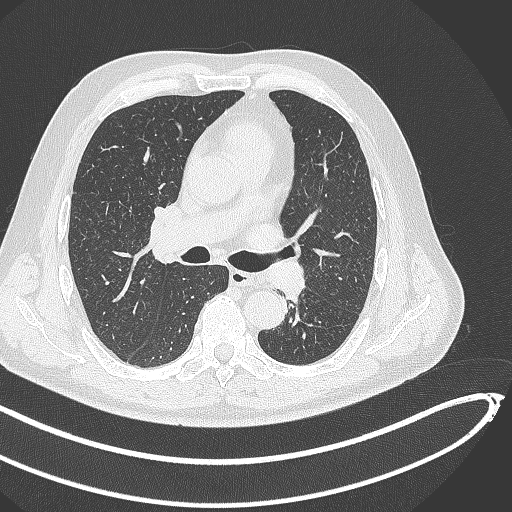
Chest CT, one axial slice; position 274 of 468 along the scan axis; reconstruction kernel B70f; 120 kVp; lung window (W 1500 / L -600 HU); 1 mm slice thickness; 512 × 512 image matrix. Patient: male, 64 years. Case-level facts recorded for this patient, not image findings: clinical TNM (as recorded): T1c N0 M0; histopathological grade: G2.
Outlined on this slice (bounding box drawn by a radiologist):
- lung tumour (recorded histology: squamous cell carcinoma): bounding box (x1, y1, x2, y2) in pixels: (269, 257, 308, 302)